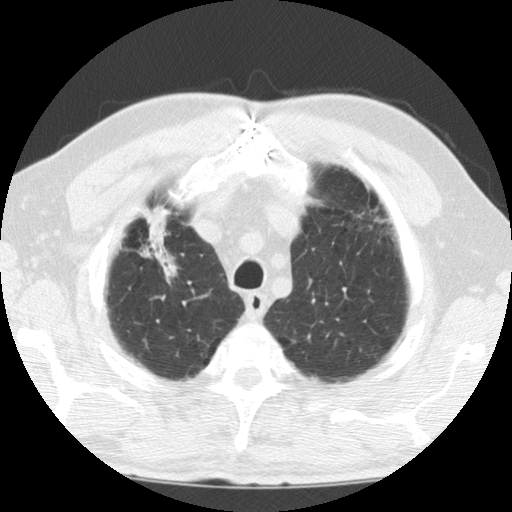
Low-dose screening chest CT, axial slice. Baseline annual screen. Lung window (W 1500 / L -600 HU). 2.5 mm slice thickness. Slice 17 of 124 in the series. Male participant, aged 69 years at enrolment. Former smoker at enrolment.
Lesion marked by an expert reader, box from (x=105, y=213) to (x=190, y=294) px. No non-calcified nodule or mass ≥4 mm was recorded by the screening reader at this exam. Lung cancer was diagnosed 171 days after this screen: adenocarcinoma, NOS, right upper lobe, poorly differentiated (G3), stage IIIB (AJCC 6th edition), 40 mm at pathology.